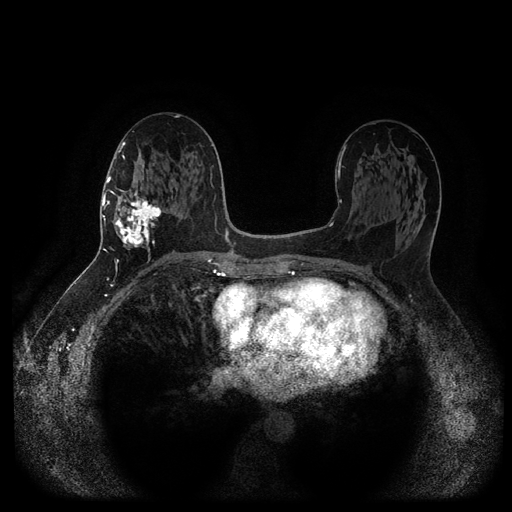
Breast MRI (dynamic contrast-enhanced, multi-phase), one axial slice; position 52 of 116 along the scan axis; dynamic contrast-enhanced series, time point 2 of 5 at this slice position (early post-contrast); 1.5 T; TE 2.6 ms, TR 5.3 ms; 2 mm slice thickness; 512 × 512 image matrix, field of view 360 × 360 mm. Patient: female, 58 years.
Structures marked on this image (semi-automatically segmented with operator editing):
- breast lesion (labelled 'tumour' in the annotation; benign lesions carry a separate 'benign' label): bounding box <112,186,164,256> (left, top, right, bottom; pixels)